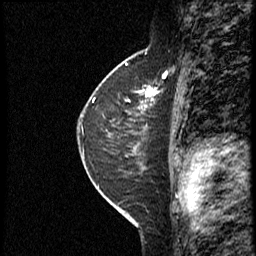
Breast MRI (dynamic contrast-enhanced), one sagittal slice. Position 23 of 40 along the scan axis. Dynamic contrast-enhanced study with each time point stored as its own series, time point 2 of 4 at this slice position (early post-contrast, ordered by acquisition time). 1.5 T. TE 4.2 ms, TR 18.8 ms. 256 × 256 image matrix, field of view 200 × 200 mm. Female patient. From the clinical record (not read from this slice): setting: breast cancer imaged before/during neoadjuvant chemotherapy; receptor status: HER2-positive.
Annotated regions visible in this slice (semi-automatically segmented with operator editing):
- analysis volume of interest (the breast-tissue region the enhancement analysis was run in; not a lesion): bounding box (x1, y1, x2, y2) in pixels: (91, 79, 167, 153)
- tumour enhancement mask (voxels above the 100 % enhancement threshold inside the analysis volume of interest): (142, 88, 156, 100)